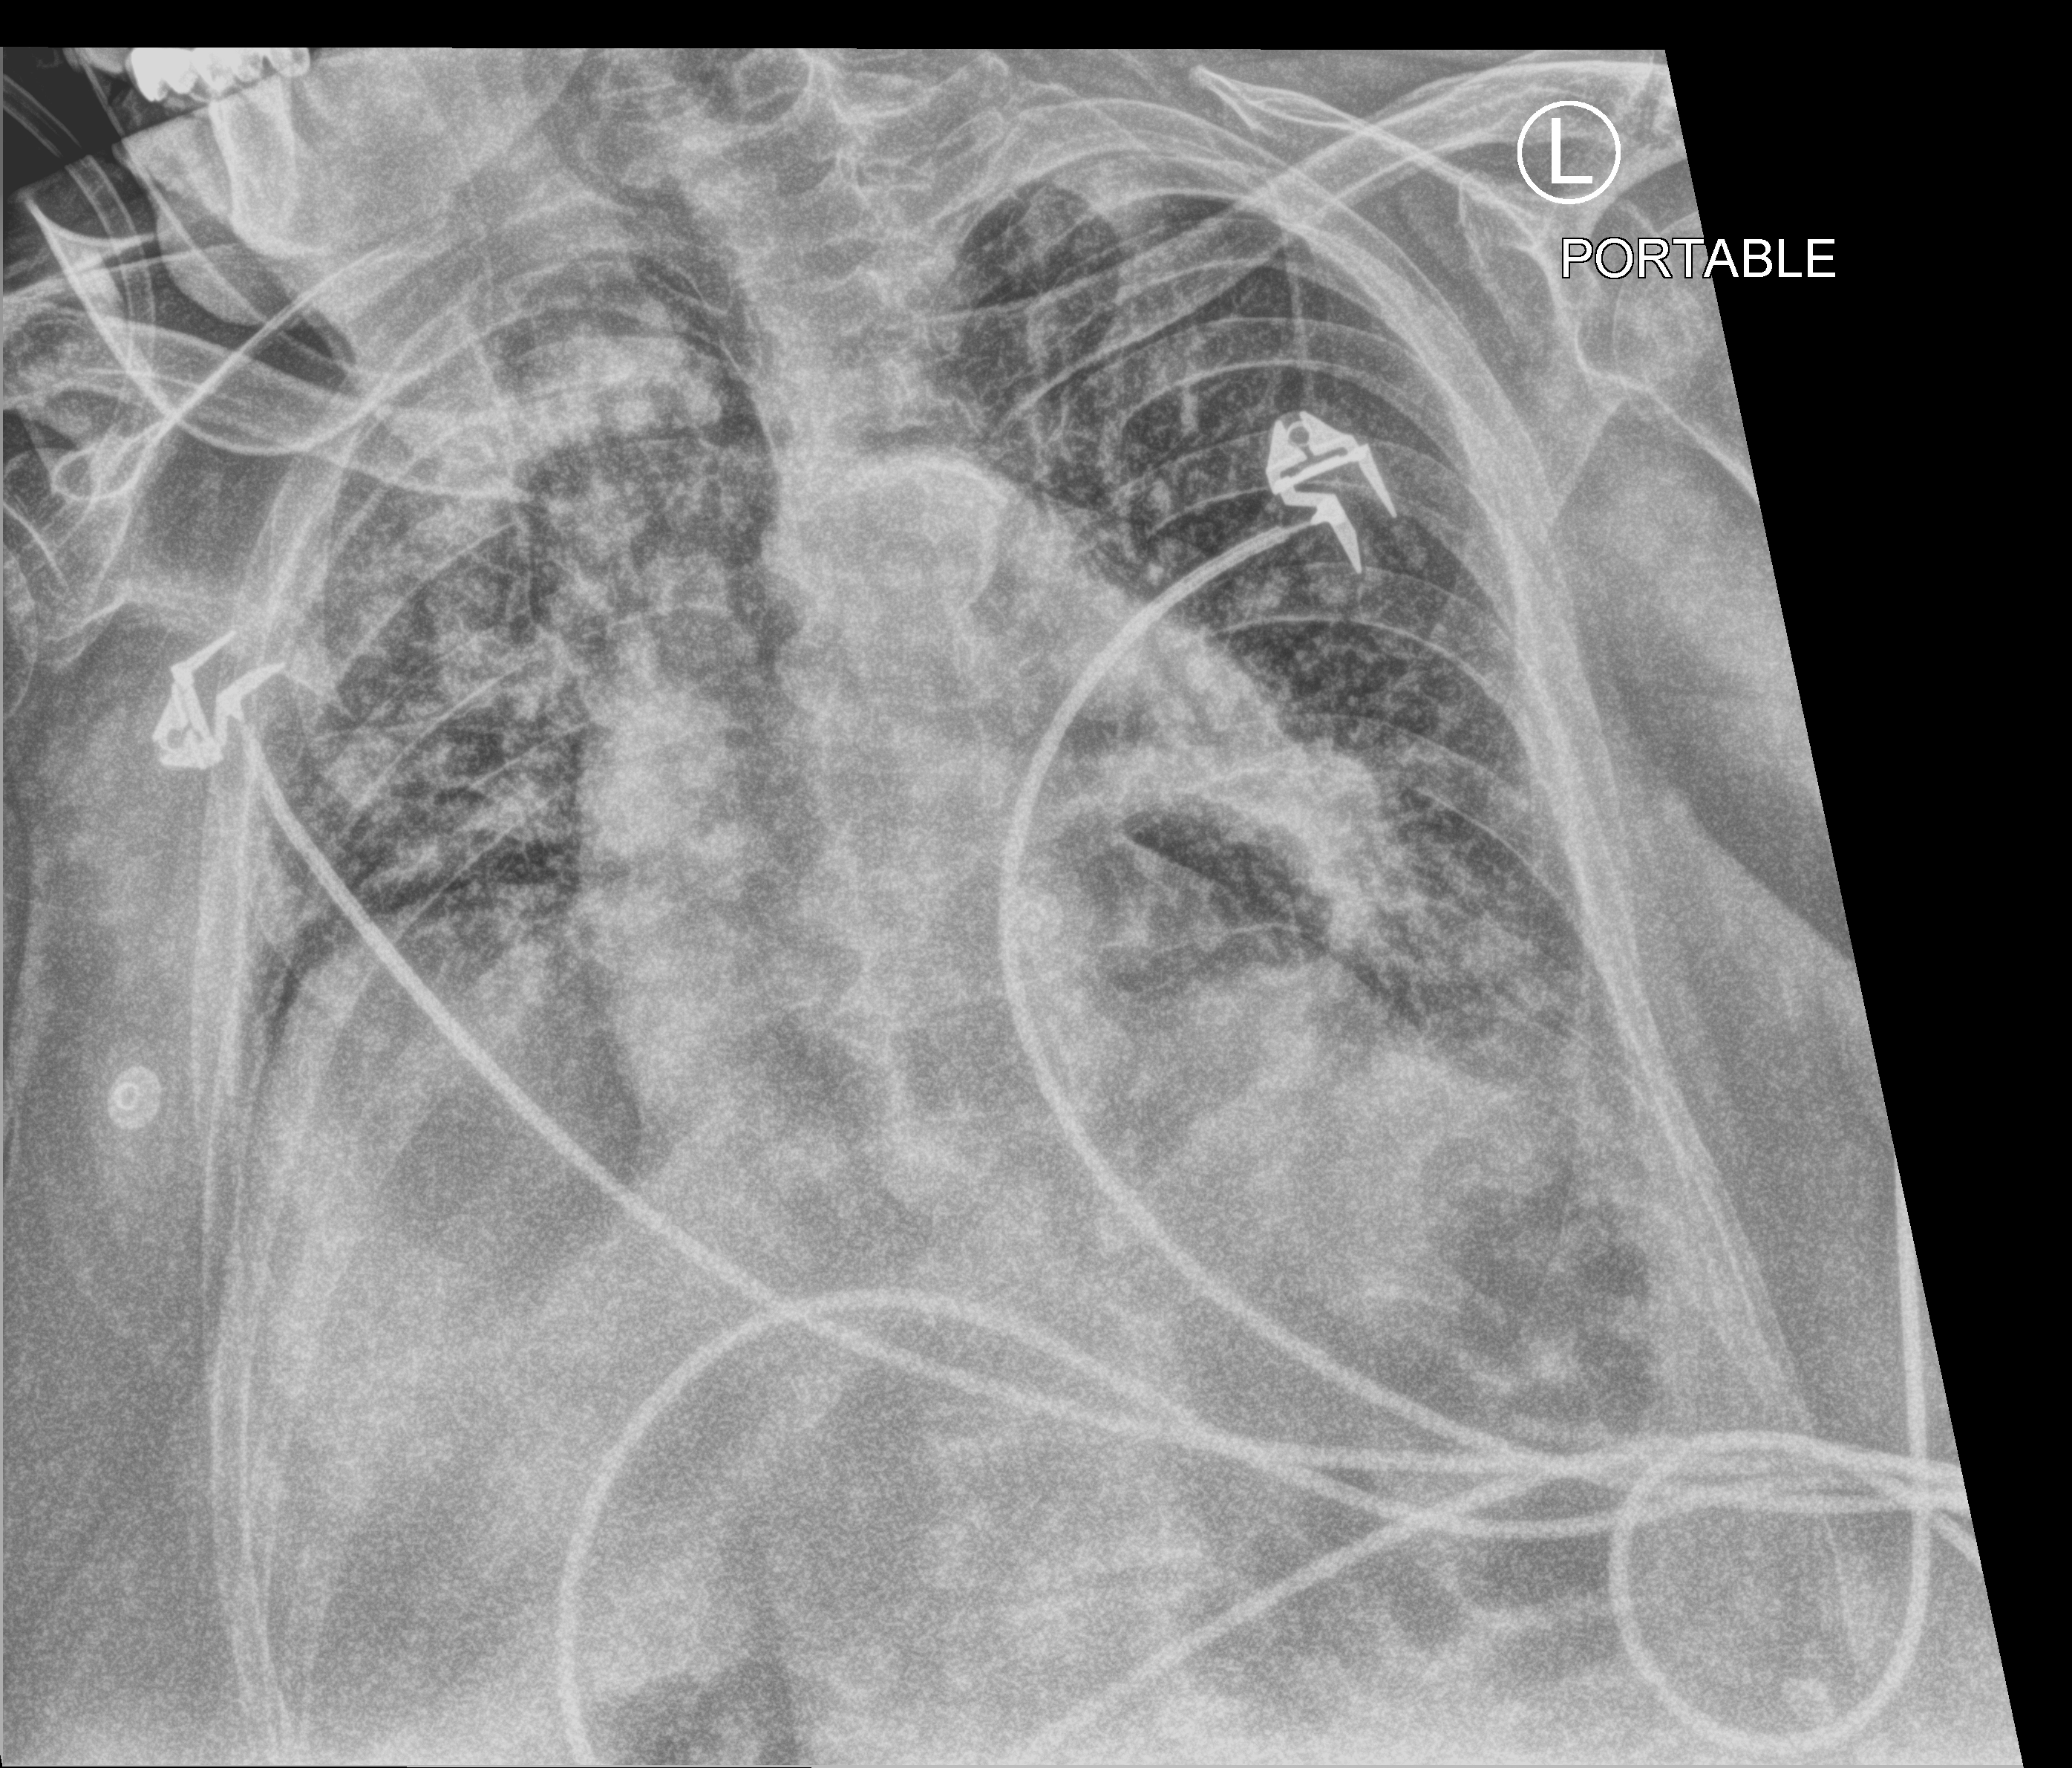
Portable chest radiograph; anteroposterior (AP) projection. Female patient hospitalised with COVID-19, age 75–90 years.
Admission-level facts for this patient (not findings on this image; timing relative to this image not recorded):
- hypertension (admission record): yes
- admitted to intensive care during this hospital stay: no
- smoking status (admission record): never